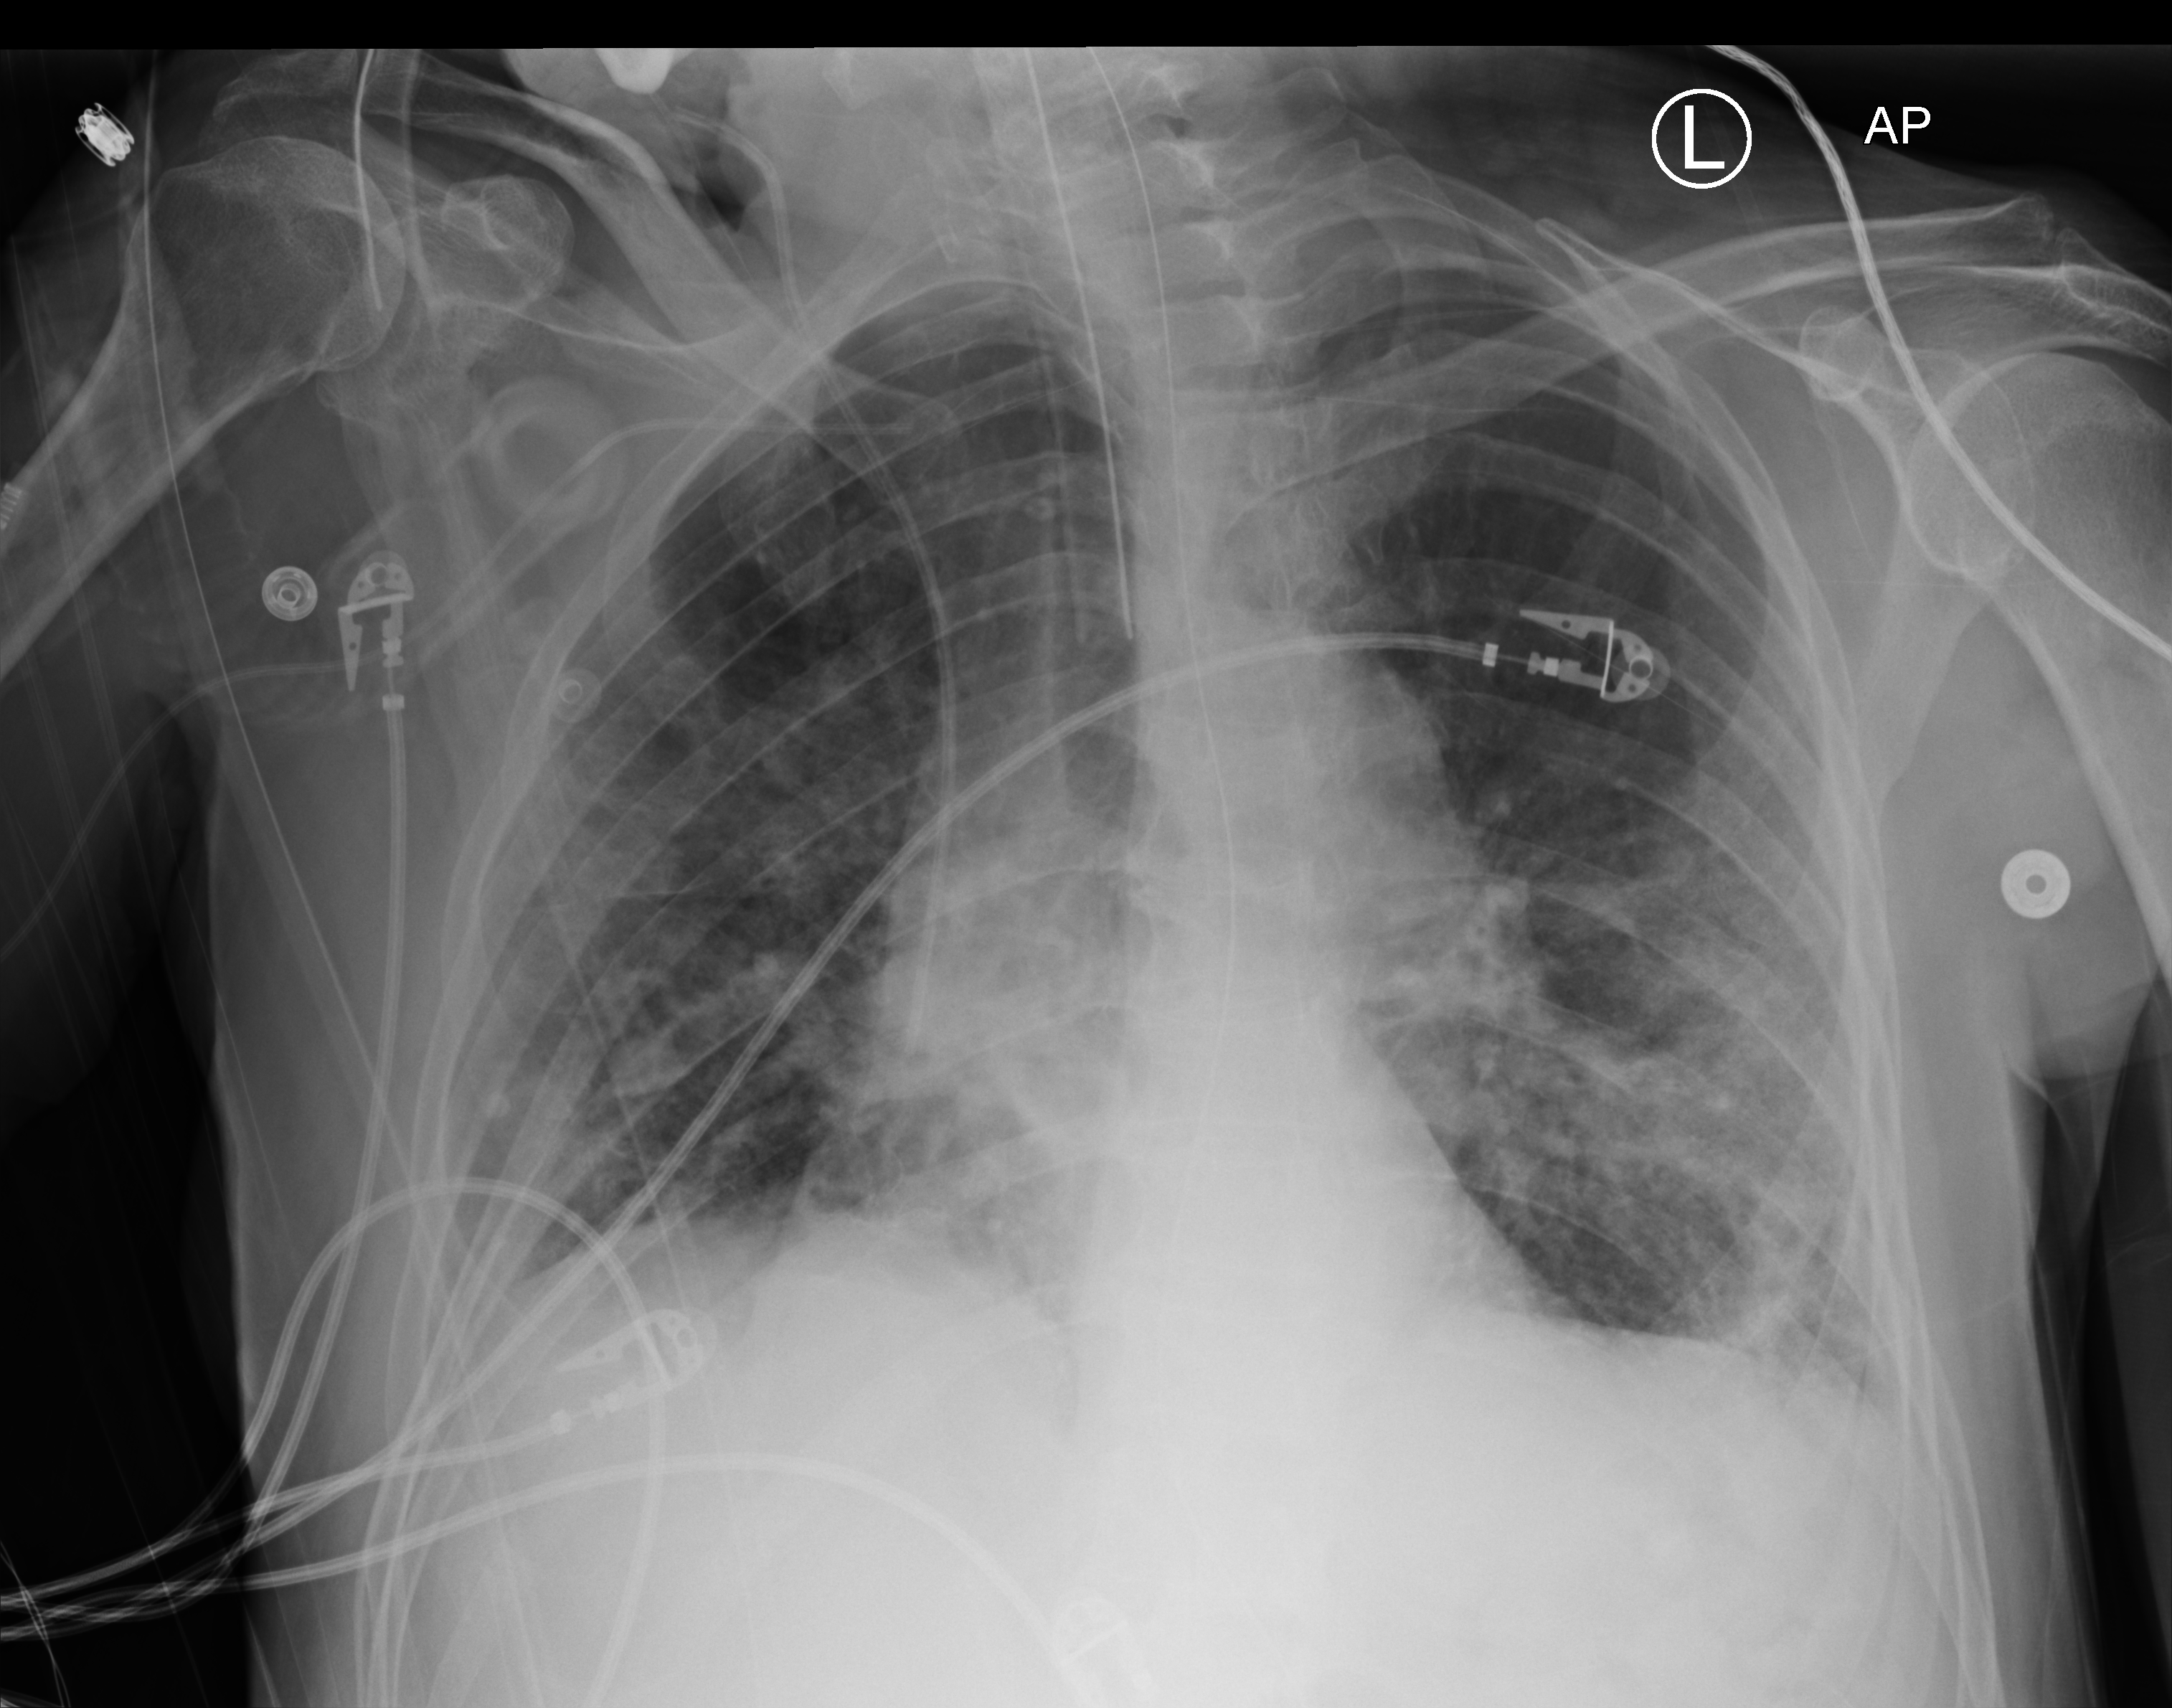
Chest X-ray (portable). Patient hospitalised with COVID-19; male, aged 75–90 years.
Hospital-stay facts (about this admission, not read from this image; timing relative to this image not recorded): length of hospital stay: 70 days; mechanically ventilated during this hospital stay: yes.